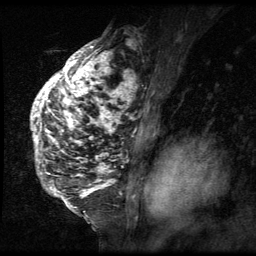
Breast MRI (dynamic contrast-enhanced), one sagittal slice. Slice 41 of 64 in the series (ordered by position). 3 images stored at this slice position (order not interpretable as contrast timing). 1.5 T. TE 4.2 ms, TR 9 ms. 2.5 mm slice thickness. 256 × 256 image matrix, field of view 180 × 180 mm. Patient: female, 50 years. From the clinical record (not read from this slice): setting: breast cancer imaged before/during neoadjuvant chemotherapy; receptor status: triple-negative.
Annotated regions visible in this slice (semi-automatically segmented with operator editing):
- analysis volume of interest (the breast-tissue region the enhancement analysis was run in; not a lesion): box from (x=30, y=39) to (x=140, y=212) px
- tumour enhancement mask (voxels above the 140 % enhancement threshold inside the analysis volume of interest): (x=31, y=40)–(x=140, y=207)